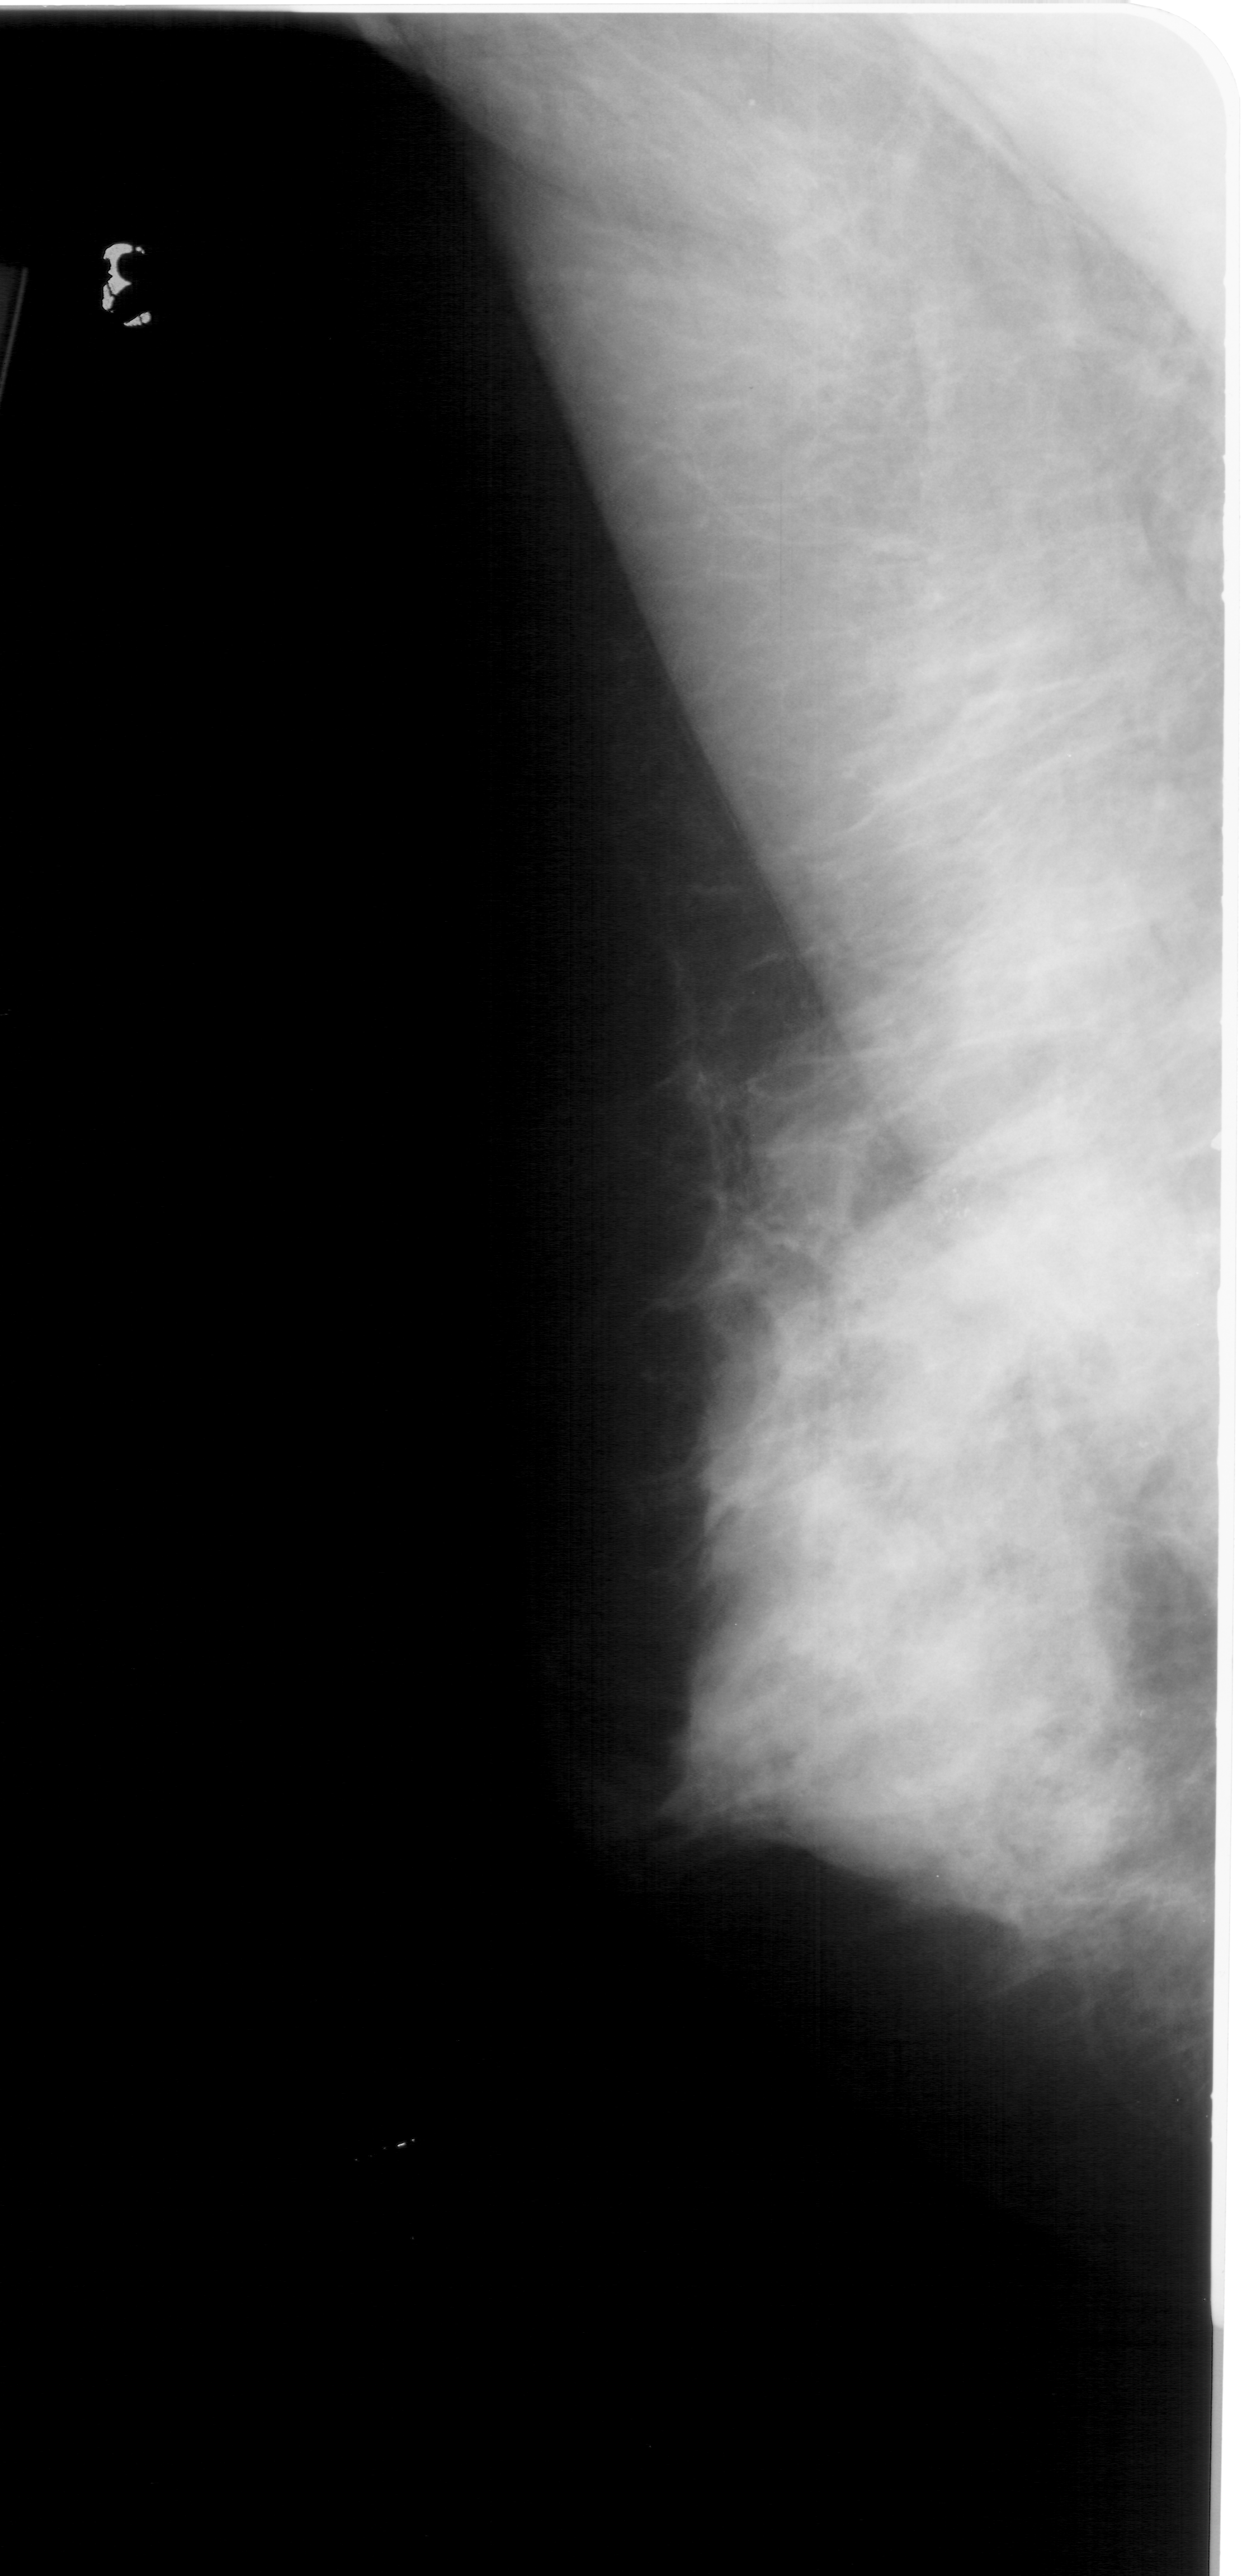
Digitized screen-film mammogram, left breast, MLO view.
- Marked findings (only marked abnormalities are described; nothing is implied about the rest of the image): calcifications, morphology pleomorphic, distribution clustered; BI-RADS assessment category 4; subtlety rating 2 on a 1 (subtle) to 5 (obvious) scale; pathology result (as recorded, not read from the image): malignant.